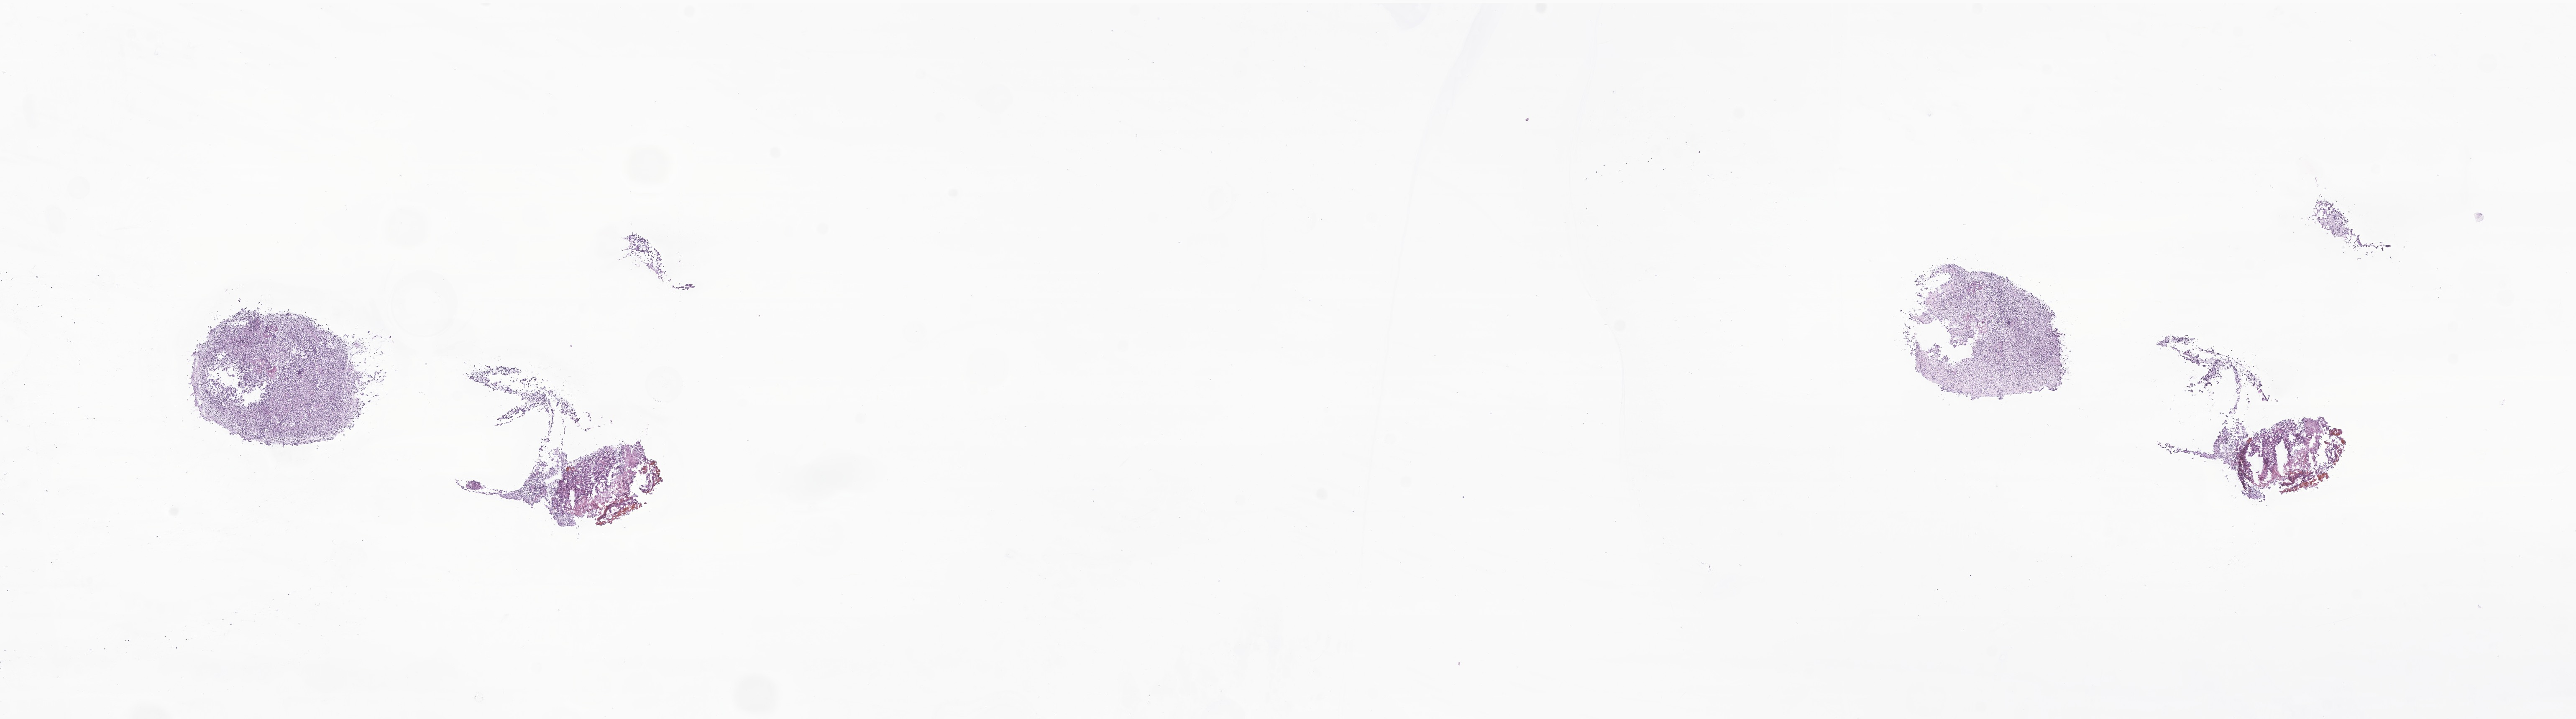
H&E whole-slide image of tumor tissue from the brain — a low-resolution overview of the entire scanned area, about 26.0 x 7.3 mm. Frozen section. Patient male; age 146 months (12 years 2 months).
Recorded diagnosis: Medulloblastoma, NOS.